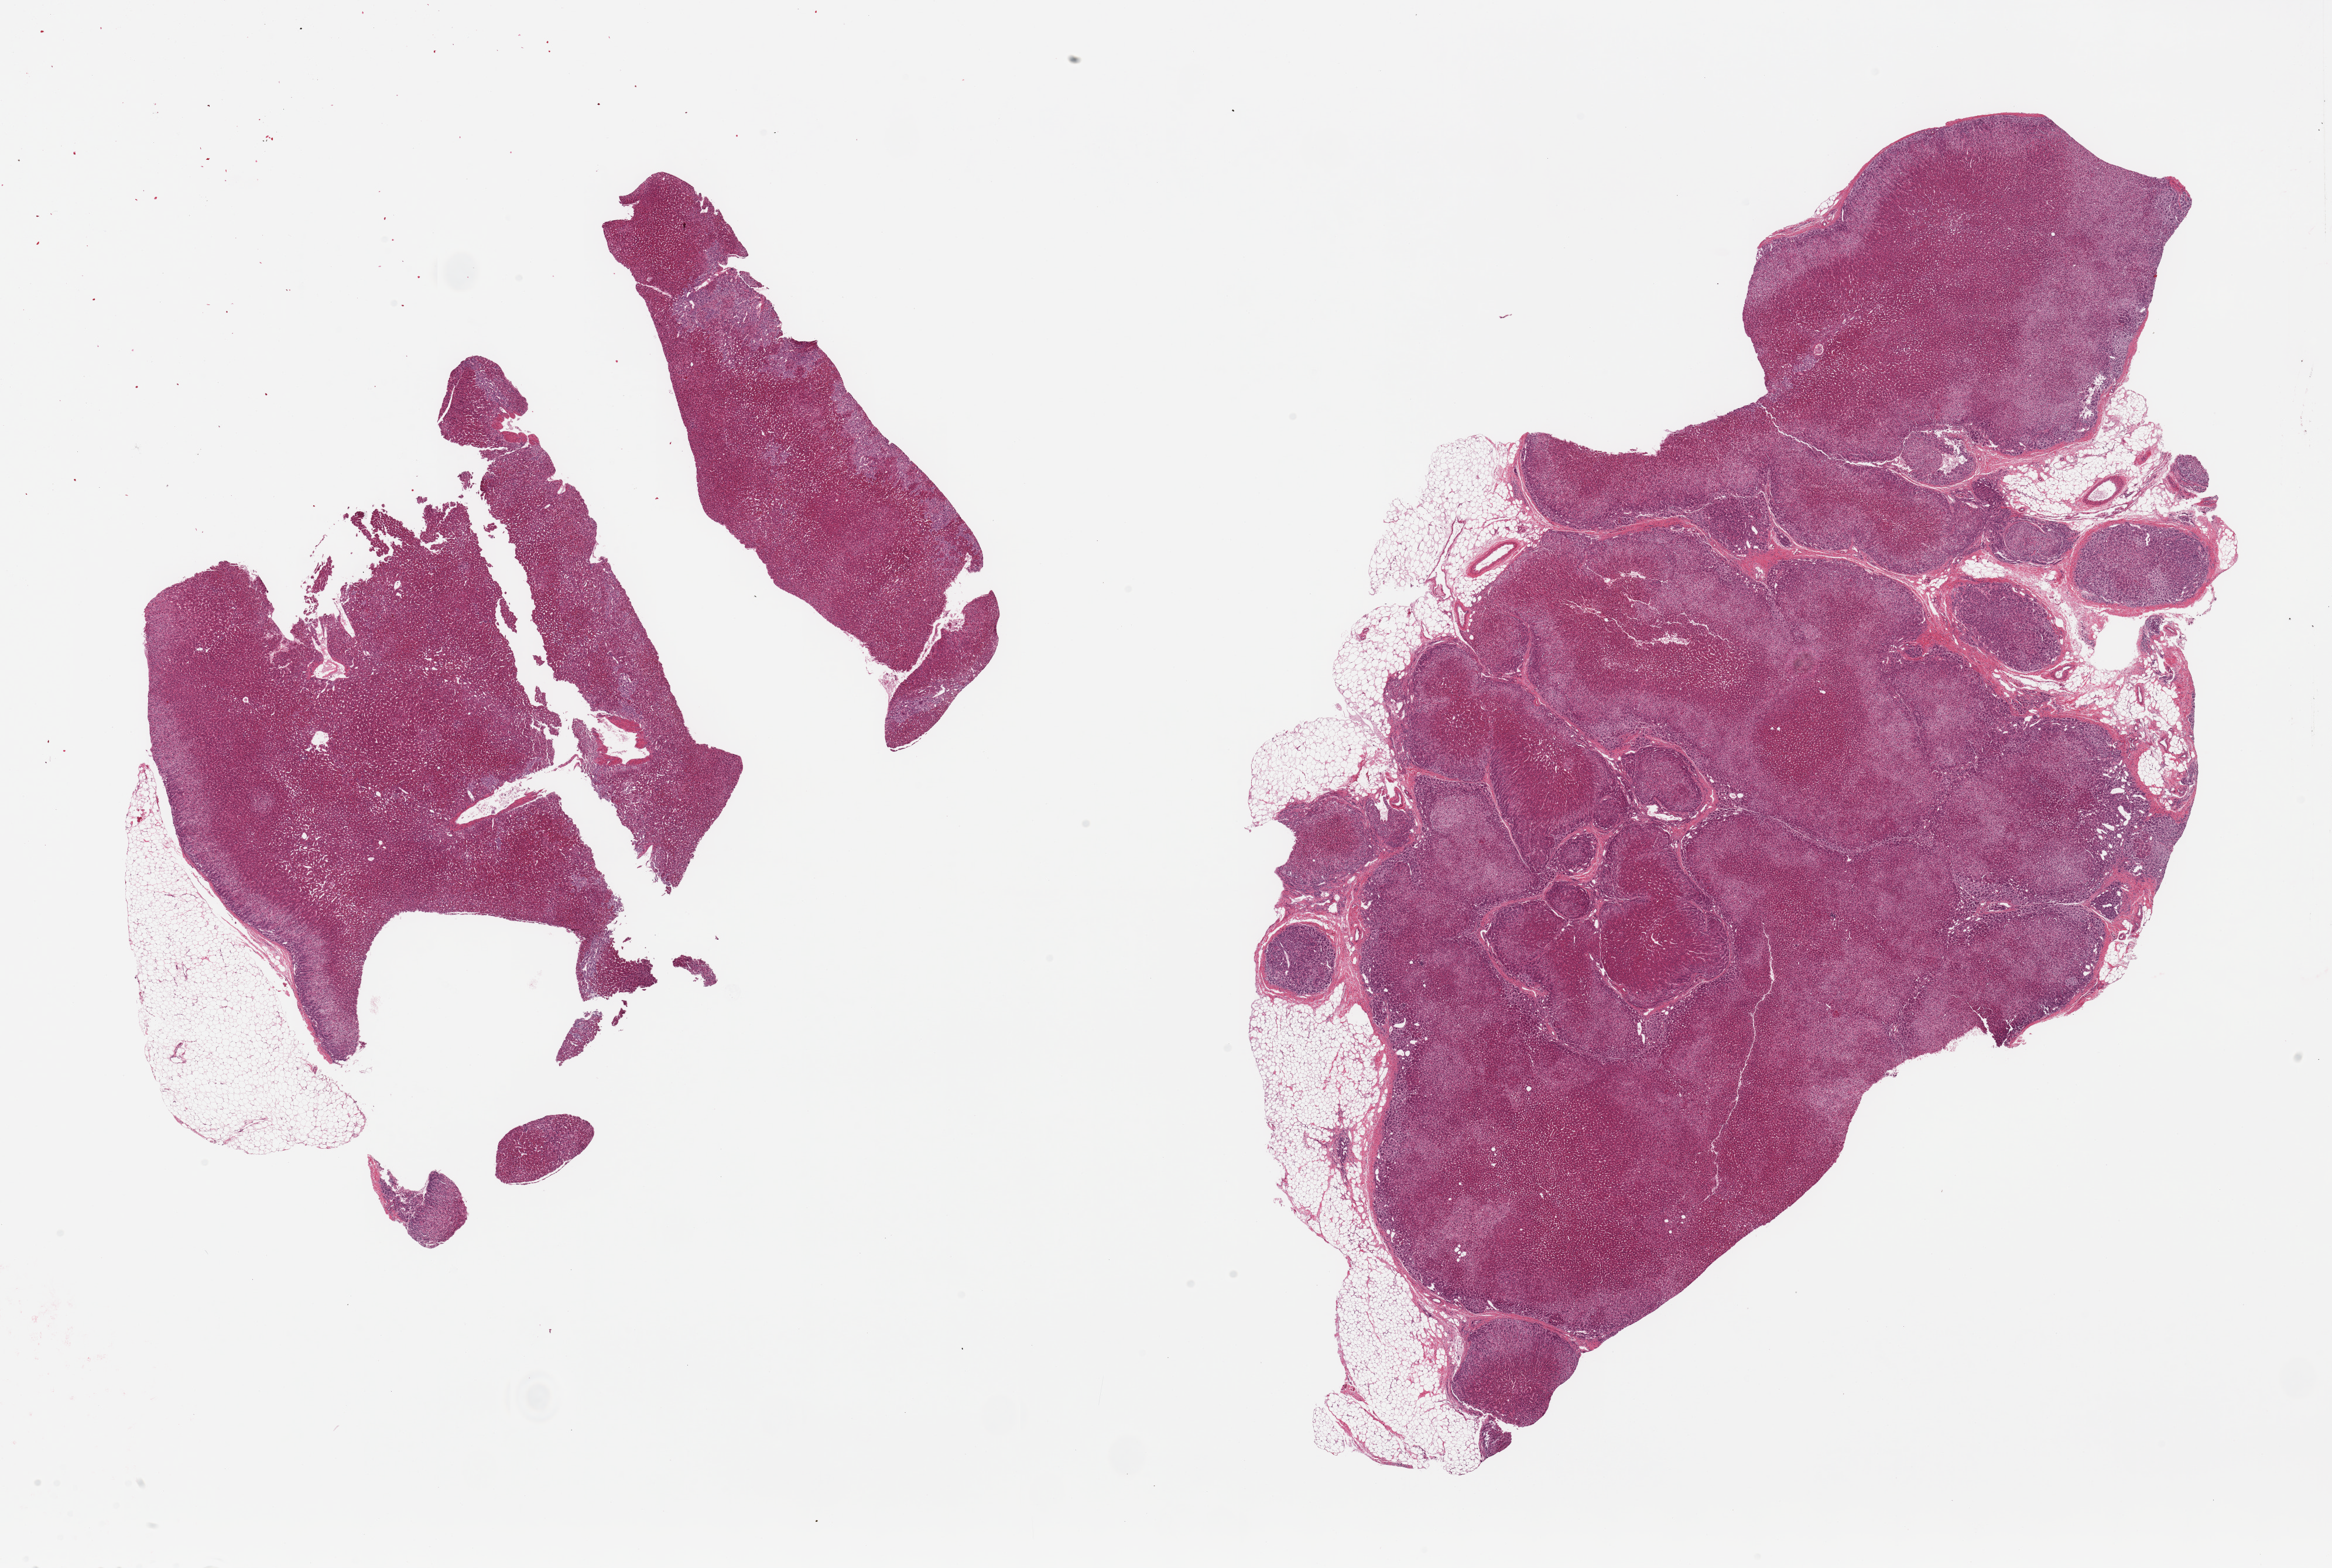
Haematoxylin and eosin whole-slide image — a low-resolution overview of the entire scanned area, about 31.5 x 21.2 mm. PAXgene-fixed, paraffin-embedded tissue. Sampled site (target tissue): adrenal gland. Tissue donor sample. Donor: male.
Review note (as recorded): 2 fragmented pieces; up to 1.6mm peripheral fat.